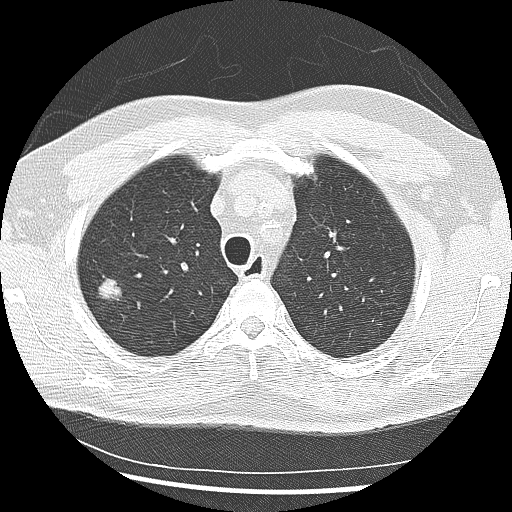
Low-dose screening chest CT, one axial slice; slice 207 of 265 in the series (ordered by position); reconstruction kernel LUNG; 120 kVp; lung window (W 1500 / L -600 HU); 2.5 mm slice thickness; 512 × 512 image matrix, field of view 340 × 340 mm.
Outlined on this slice (expert manual segmentation):
- lesion 1 (tumor, upper lobe of right lung): bounding box [x1, y1, x2, y2] px = [98, 279, 122, 299]